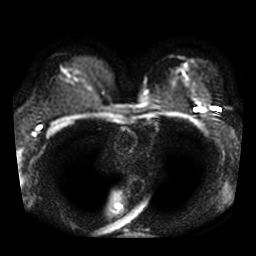
Breast MRI, one axial slice; slice 26 of 38 in the series (ordered by position); diffusion-weighted series; image 2 of 4 stored at this slice position (different b-values; order by instance number); 3 T; 5 mm slice thickness; 256 × 256 image matrix. Female patient.
Outlined on this slice (manually delineated by an expert):
- tumour on diffusion-weighted imaging: bounding box (x1, y1, x2, y2) in pixels: (200, 108, 204, 113)